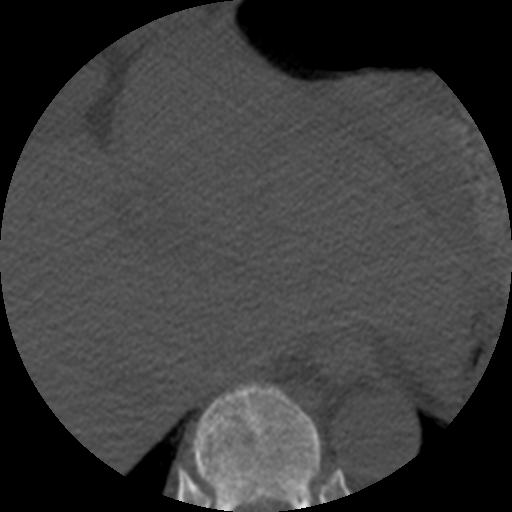
CT including the spine, one axial slice. Position 275 of 508 along the scan axis. Reconstruction kernel STANDARD. 120 kVp. Bone window (W 1800 / L 400 HU). 1.25 mm slice thickness. 512 × 512 image matrix, field of view 160 × 160 mm. Patient age 57 years. From the clinical record (not read from this slice): primary cancer: prostate.
Outlined on this slice (semi-automatically segmented with operator editing):
- T10 vertebra: box from (x=193, y=383) to (x=320, y=512) px